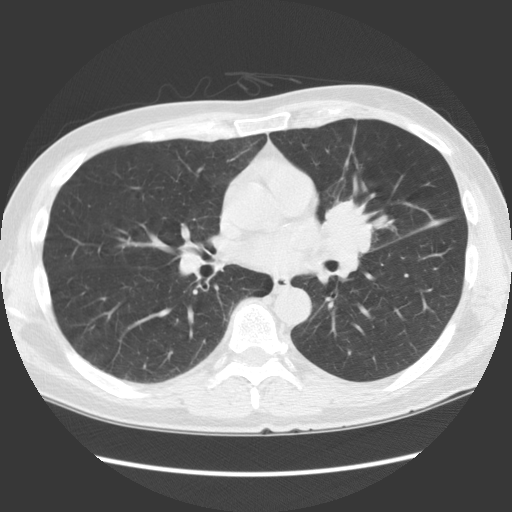
Low-dose screening chest CT, axial slice; first (baseline) screen; lung window (W 1500 / L -600 HU); 2.5 mm slice thickness; 512 × 512 image matrix, field of view 360 × 360 mm. Male, age 61 years at enrolment.
- Expert reader's lesion annotation, bounding box <298,189,395,289> (left, top, right, bottom; pixels).
- Screening reader's record for this exam (one nodule recorded; not confirmed to be the boxed lesion): non-calcified nodule or mass ≥4 mm, lingula, 35 × 35 mm, spiculated (stellate) margins, soft tissue attenuation.
- Lung cancer was diagnosed 58 days after this screen: squamous cell carcinoma, NOS, left hilum, left main stem bronchus, poorly differentiated (G3), stage IA (AJCC 6th edition), 40 mm at pathology.